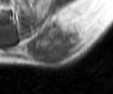
MRI of an extremity soft-tissue mass, one axial slice; slice 29 of 42 in the series (ordered by position); MR volume resampled by the dataset authors to the PET/CT grid (not the native acquisition matrix); 3.27 mm slice thickness; 113 × 94 image matrix. Male patient. Case-level facts recorded for this patient, not image findings: histological type: leiomyosarcoma; grade: intermediate; site of the primary tumour: left pelvis.
Outlined on this slice (expert contour drawn on MRI and transferred to this co-registered scan by the dataset authors):
- gross tumour volume (mass): bounding box [x1, y1, x2, y2] px = [26, 20, 87, 67]